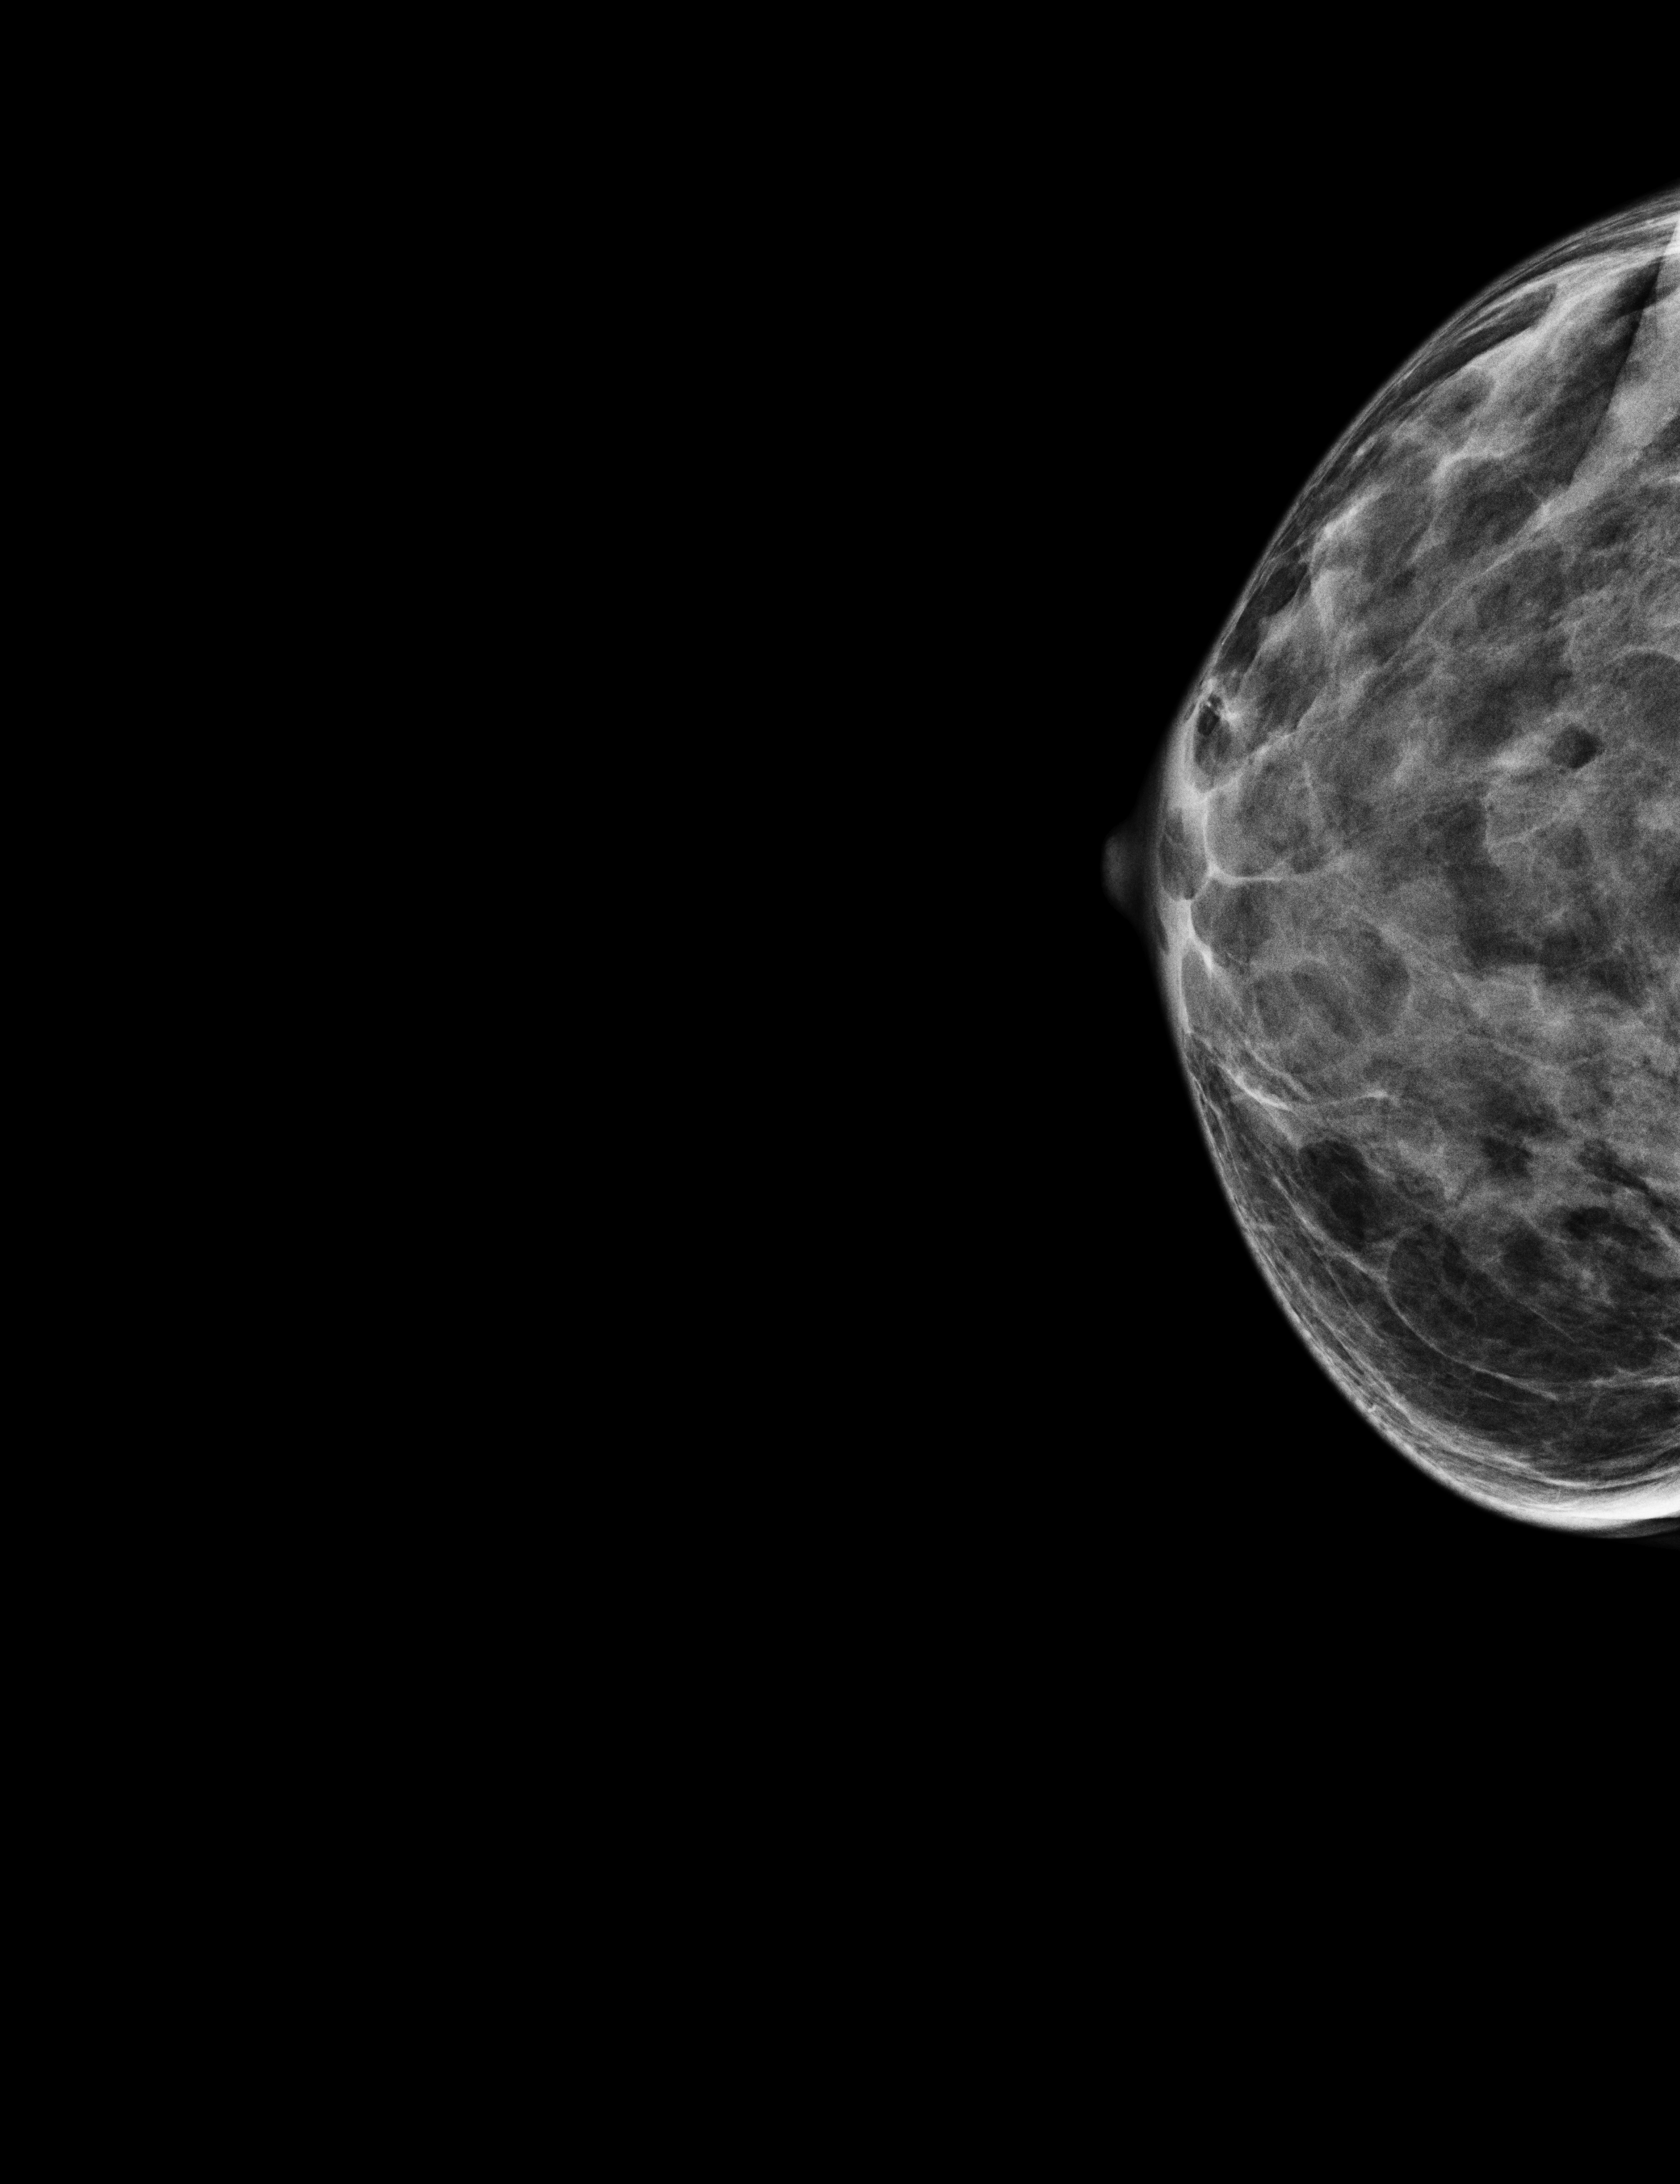
Annual screening mammography examination; compressed breast thickness 22 mm. Patient aged 69 years (female).
Image type: full-field digital mammogram. Breast: right. Projection: craniocaudal (CC) view.